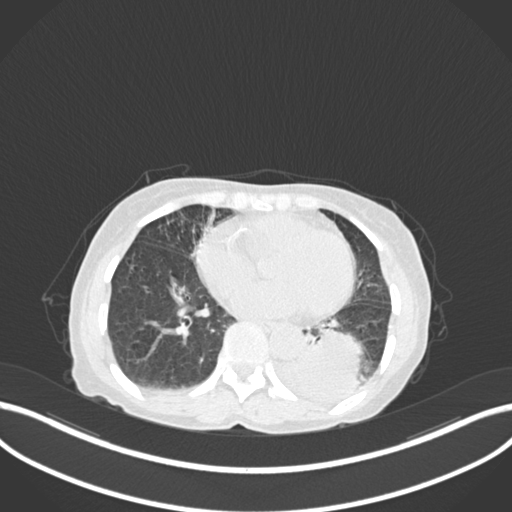
Chest CT, one axial slice; position 46 of 233 along the scan axis; 120 kVp; lung window (W 1500 / L -600 HU); 1 mm slice thickness; 512 × 512 image matrix. Female patient, age 78 years. Case-level facts recorded for this patient, not image findings: clinical TNM (as recorded): T3 N0 M1.
Outlined on this slice (bounding box drawn by a radiologist):
- lung tumour (recorded histology: squamous cell carcinoma): bounding box <272,322,368,399> (left, top, right, bottom; pixels)